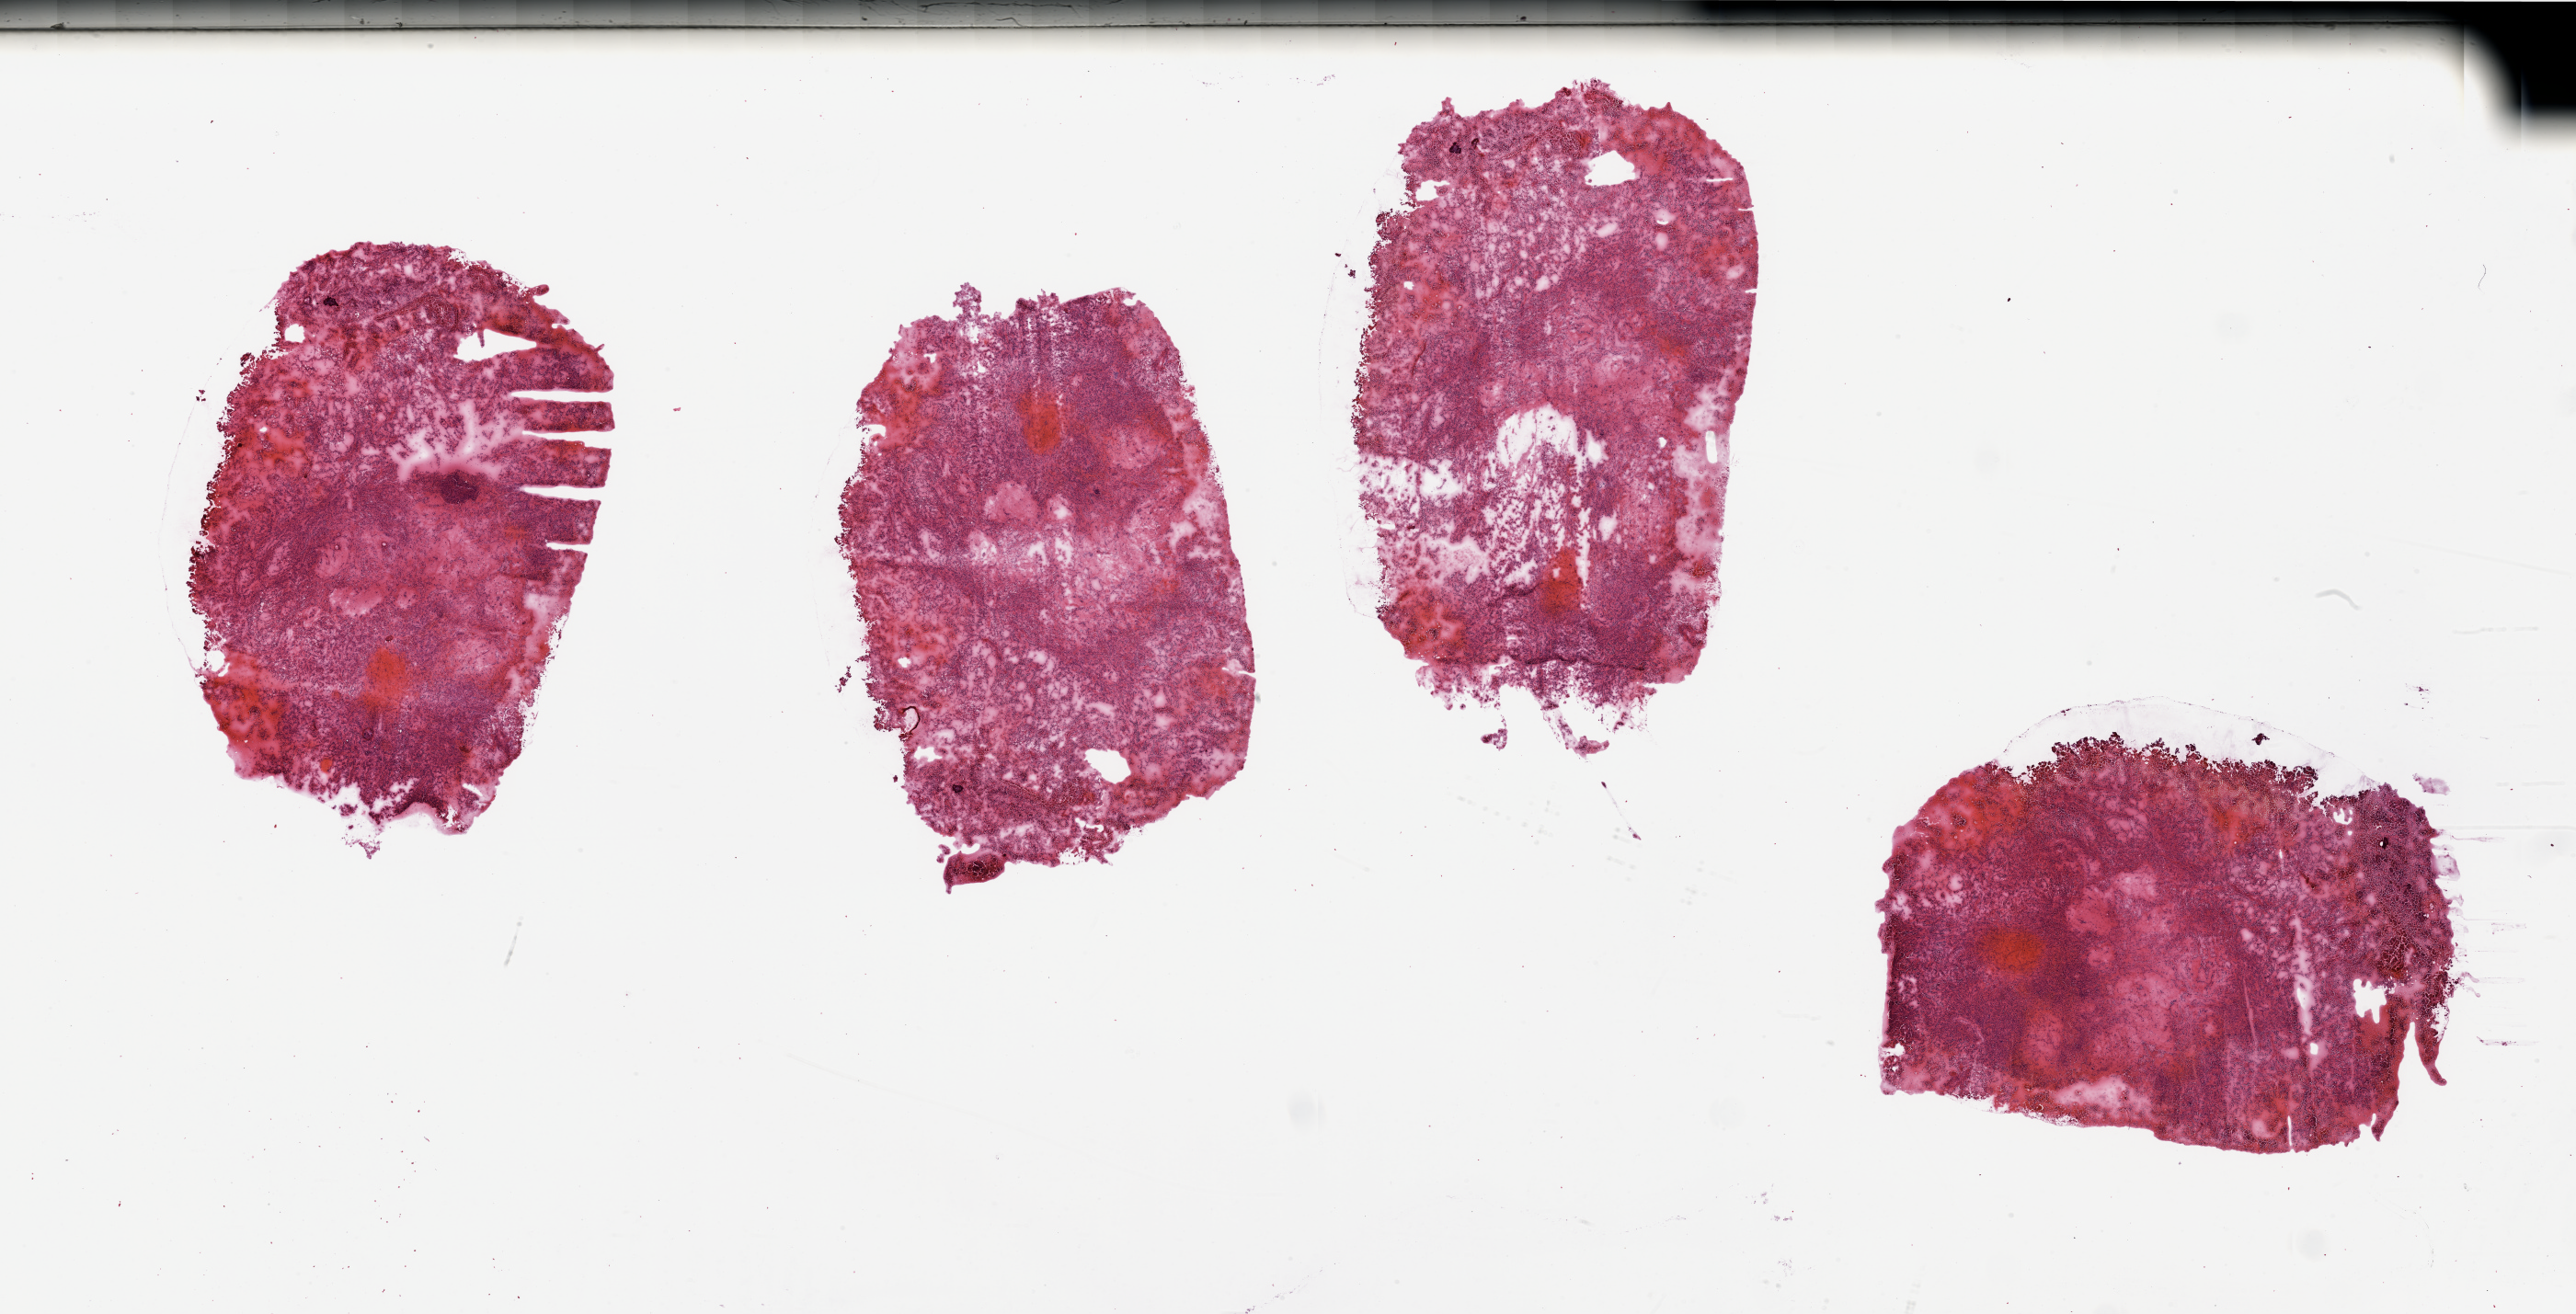
H&E-stained whole-slide image, shown as a low-resolution overview of the whole scanned area (about 44.3 x 22.6 mm, acquisition: 20x scan), kidney, tumour tissue. Patient: female, age 31 years. Histologic grade: G2 (moderately differentiated).
* histologic diagnosis: Renal cell carcinoma, NOS
* primary tumour site (as recorded): middle
* AJCC pathologic stage: I